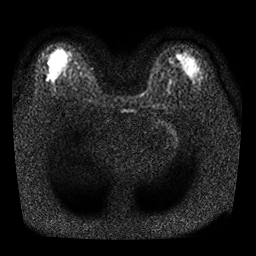
Breast MRI, one axial slice. Slice 18 of 25 in the series (ordered by position). Diffusion-weighted series; image 2 of 4 stored at this slice position (different b-values; order by instance number). 1.5 T. 4 mm slice thickness. 256 × 256 image matrix. Female patient.
Outlined on this slice (outlined manually by an expert reader):
- tumour on diffusion-weighted imaging: bounding box <50,62,52,64> (left, top, right, bottom; pixels)